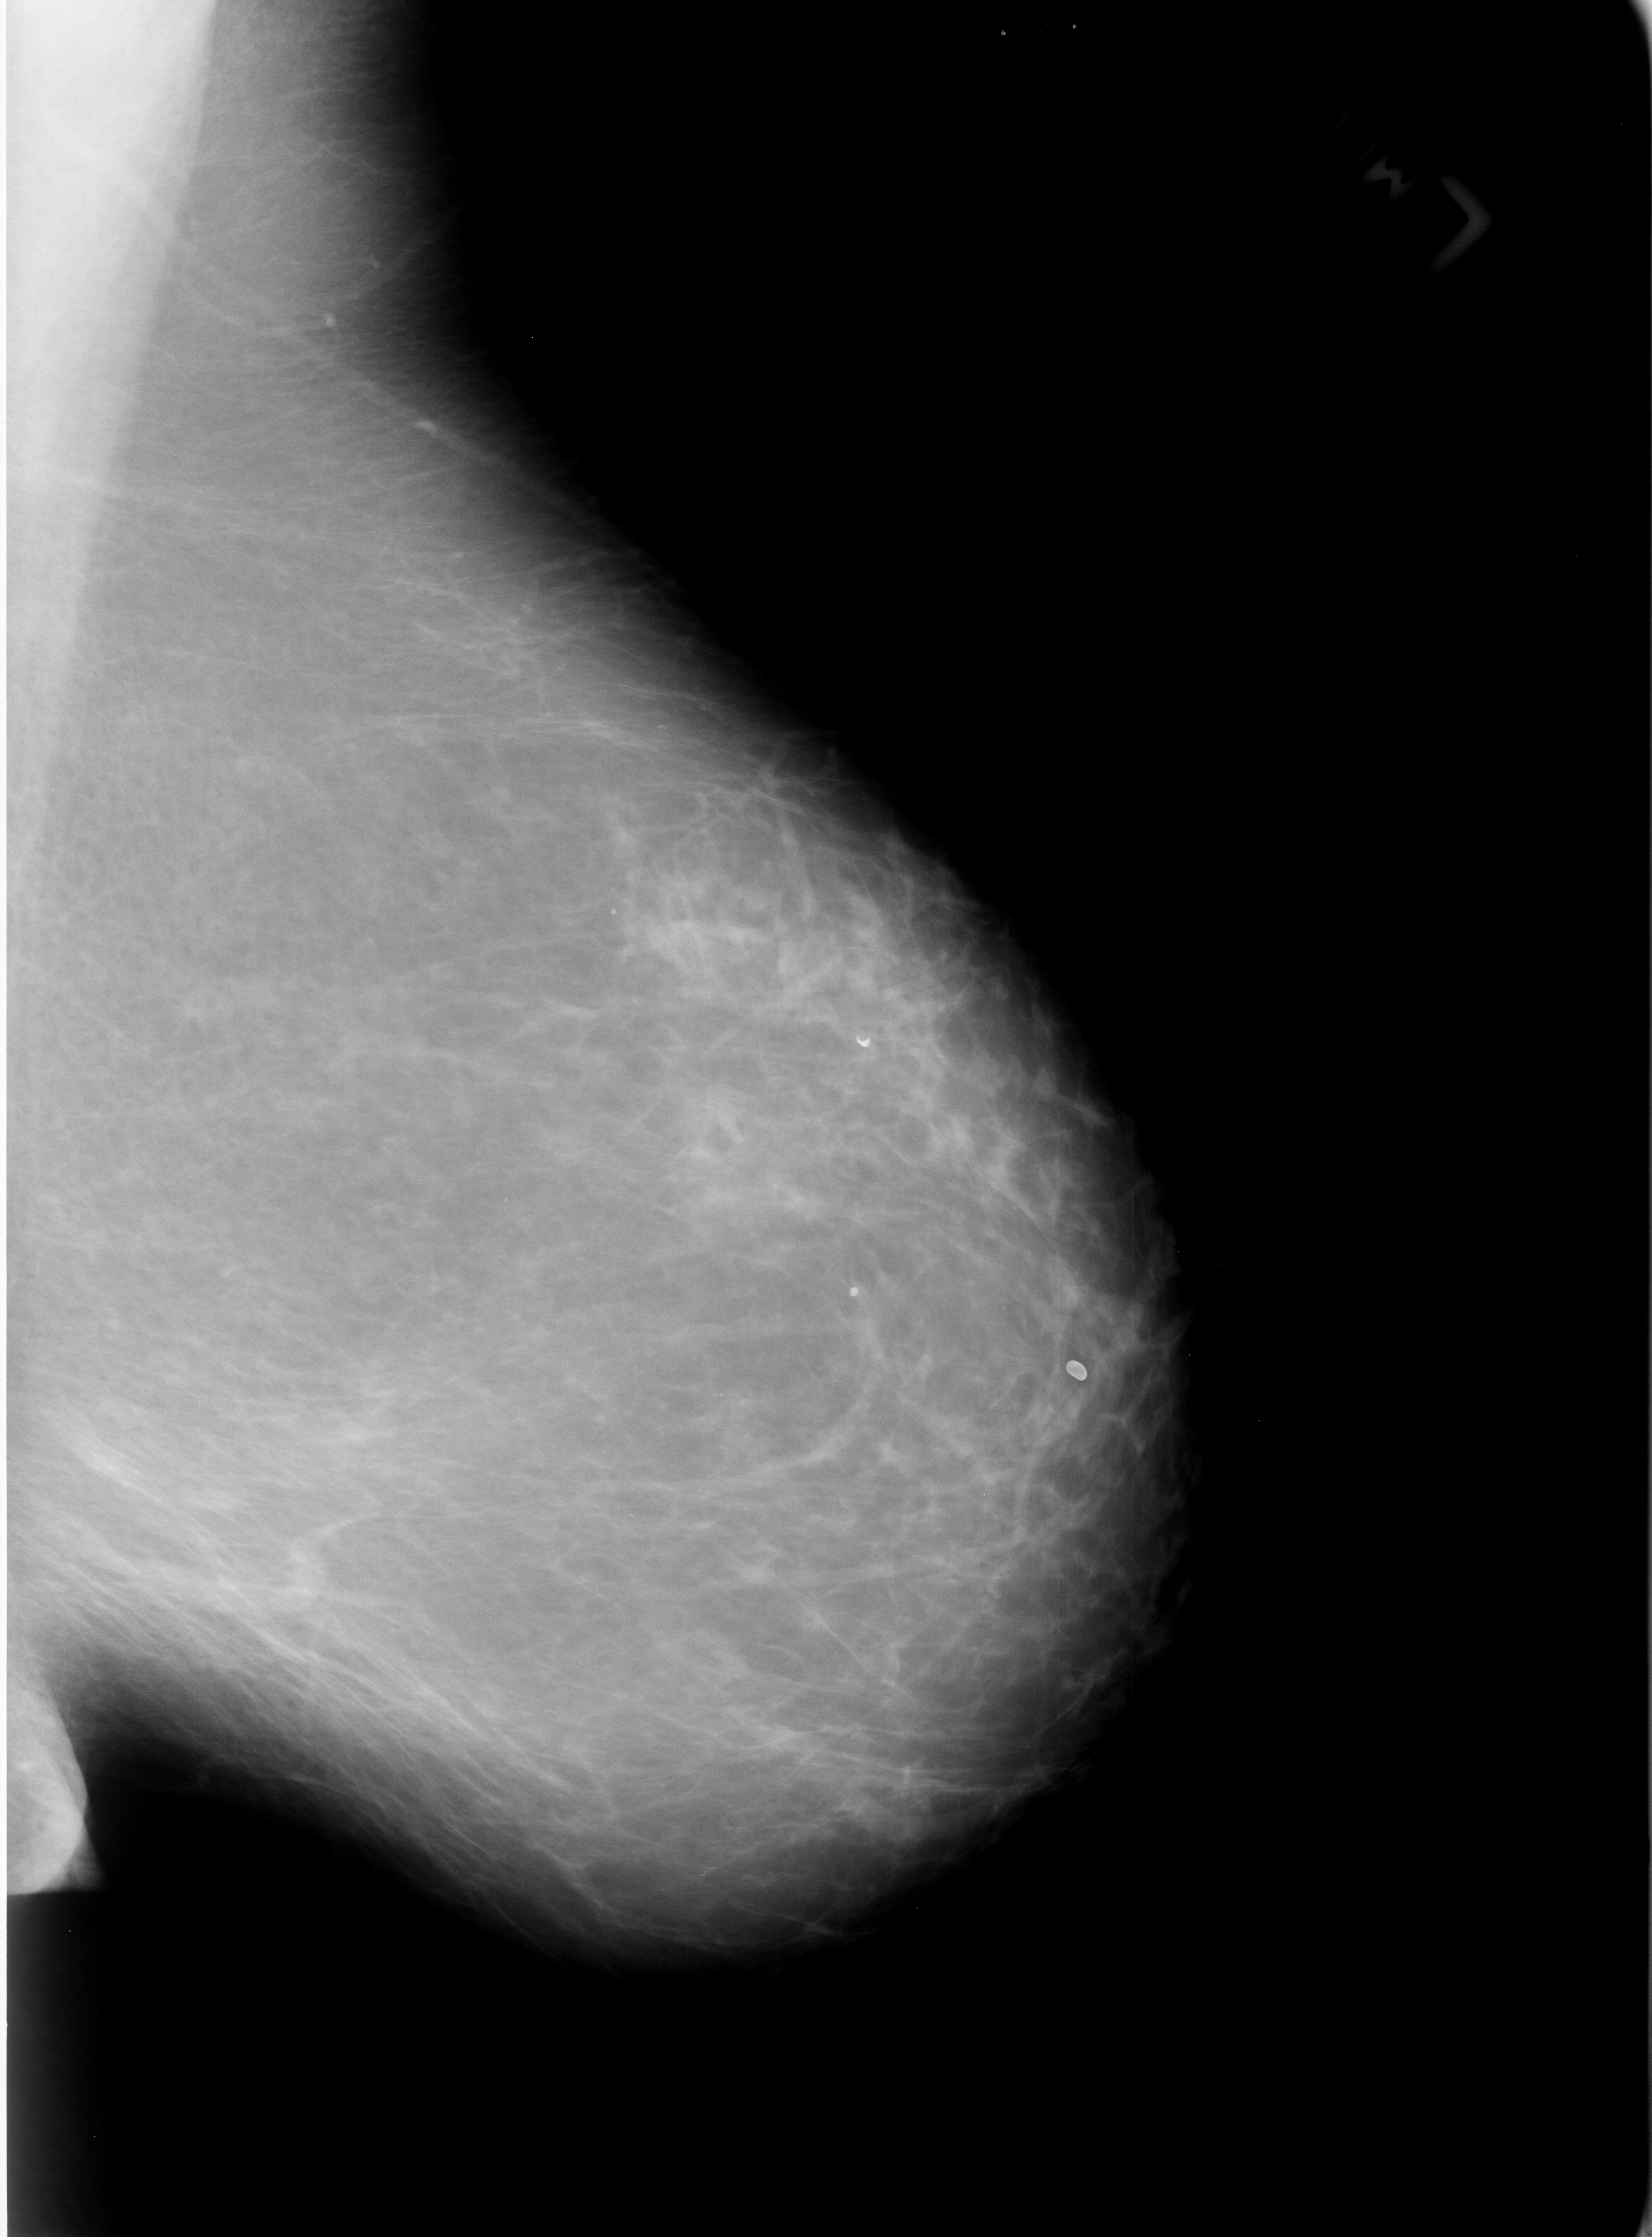
Scanned film-screen mammogram, left breast, mediolateral oblique (MLO) view, breast composition: scattered fibroglandular densities (BI-RADS density category 2 of 4).
Radiologist-marked abnormalities on this image: Finding 1 of 3: calcifications, morphology lucent center; BI-RADS assessment category 2; subtlety rating 5 on a 1 (subtle) to 5 (obvious) scale; benign without callback (not worked up further). Finding 2 of 3: calcifications, morphology lucent center; BI-RADS assessment category 2; benign without callback (not worked up further). Finding 3 of 3: calcifications, morphology lucent center; BI-RADS assessment category 2; benign without callback (not worked up further).